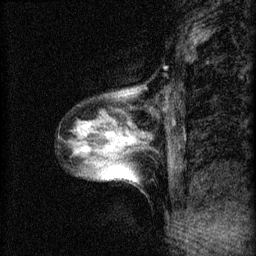
Breast MRI (dynamic contrast-enhanced), one sagittal slice; position 15 of 60 along the scan axis; 3 images stored at this slice position (order not interpretable as contrast timing); 1.5 T; TE 4.2 ms, TR 8.2 ms; 256 × 256 image matrix, field of view 180 × 180 mm. Patient: female, 40 years.
Annotated regions visible in this slice (semi-automatic segmentation, software-assisted and operator-edited):
- analysis volume of interest (the breast-tissue region the enhancement analysis was run in; not a lesion): box from (x=65, y=86) to (x=150, y=187) px
- tumour enhancement mask (voxels above the 70 % enhancement threshold inside the analysis volume of interest): (x=85, y=124)–(x=135, y=149)